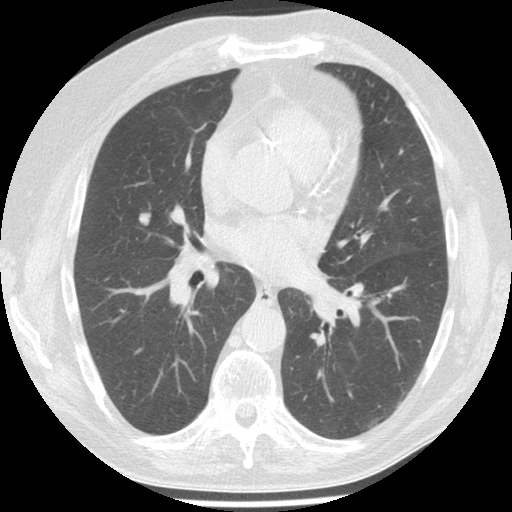
Low-dose screening chest CT, one axial slice. Position 73 of 149 along the scan axis. Lung window (W 1500 / L -600 HU). 2.5 mm slice thickness. 512 × 512 image matrix, field of view 340 × 340 mm.
Outlined on this slice (expert manual segmentation):
- lesion 1 (tumor, middle lobe of right lung): bounding box [x1, y1, x2, y2] px = [139, 213, 151, 226]